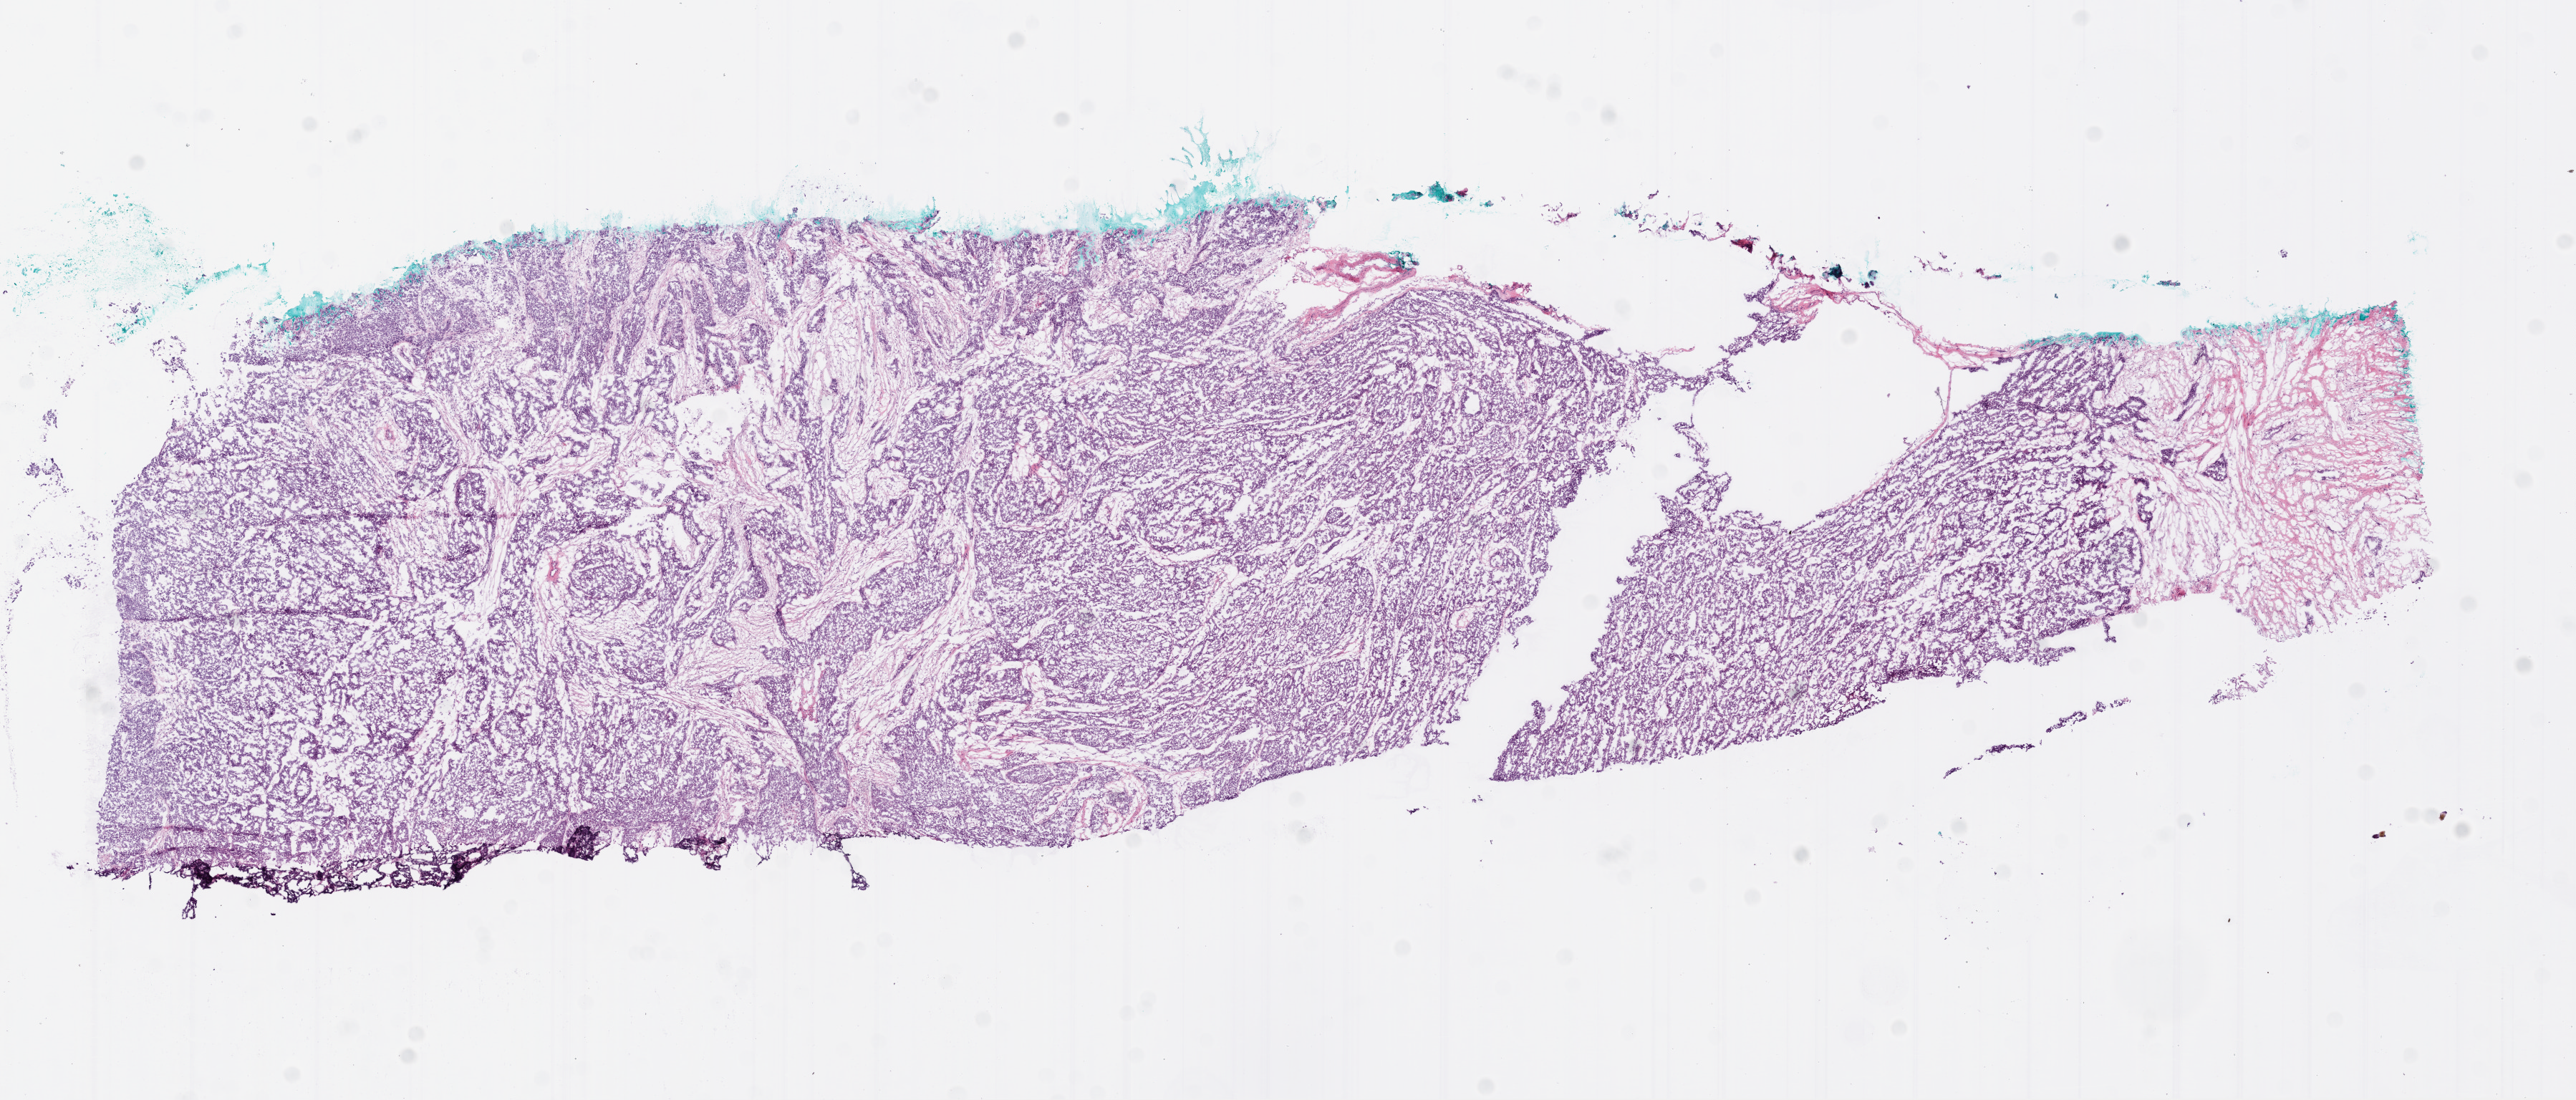
Digitized H&E-stained tissue section (whole slide), shown as a low-resolution overview of the whole scanned area (about 14.5 x 6.2 mm). Frozen section from the bottom of the tissue portion. Ovary, primary tumour sample. Female patient; age at initial diagnosis 72 years. Histologic grade: G3 (poorly differentiated). Composition of this section per pathologist review: tumour cells 90%, tumour nuclei 95%, normal cells 0%, stromal cells 10%, necrosis 0%.
FIGO stage: IV. Histologic diagnosis: Serous cystadenocarcinoma, NOS.